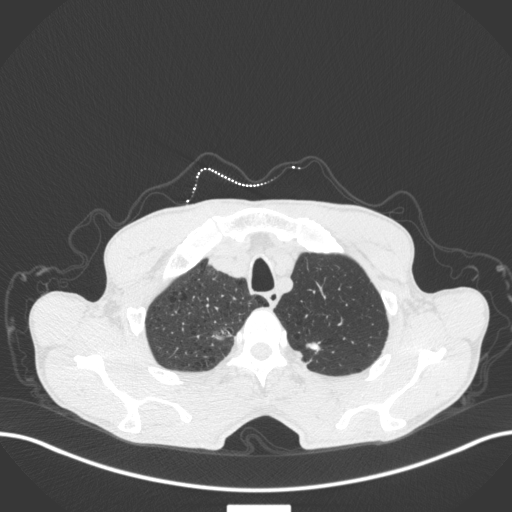
Chest CT, one axial slice. Slice 376 of 445 in the series (ordered by position). Lung window (W 1500 / L -600 HU). 1 mm slice thickness. 512 × 512 image matrix, field of view 400 × 400 mm. Male patient, age 70 years. Case-level facts recorded for this patient, not image findings: clinical TNM (as recorded): T1a N0 M0; histopathological grade: G1-2.
Outlined on this slice (bounding box drawn by a radiologist):
- lung tumour (recorded histology: adenocarcinoma): box from (x=209, y=320) to (x=234, y=346) px